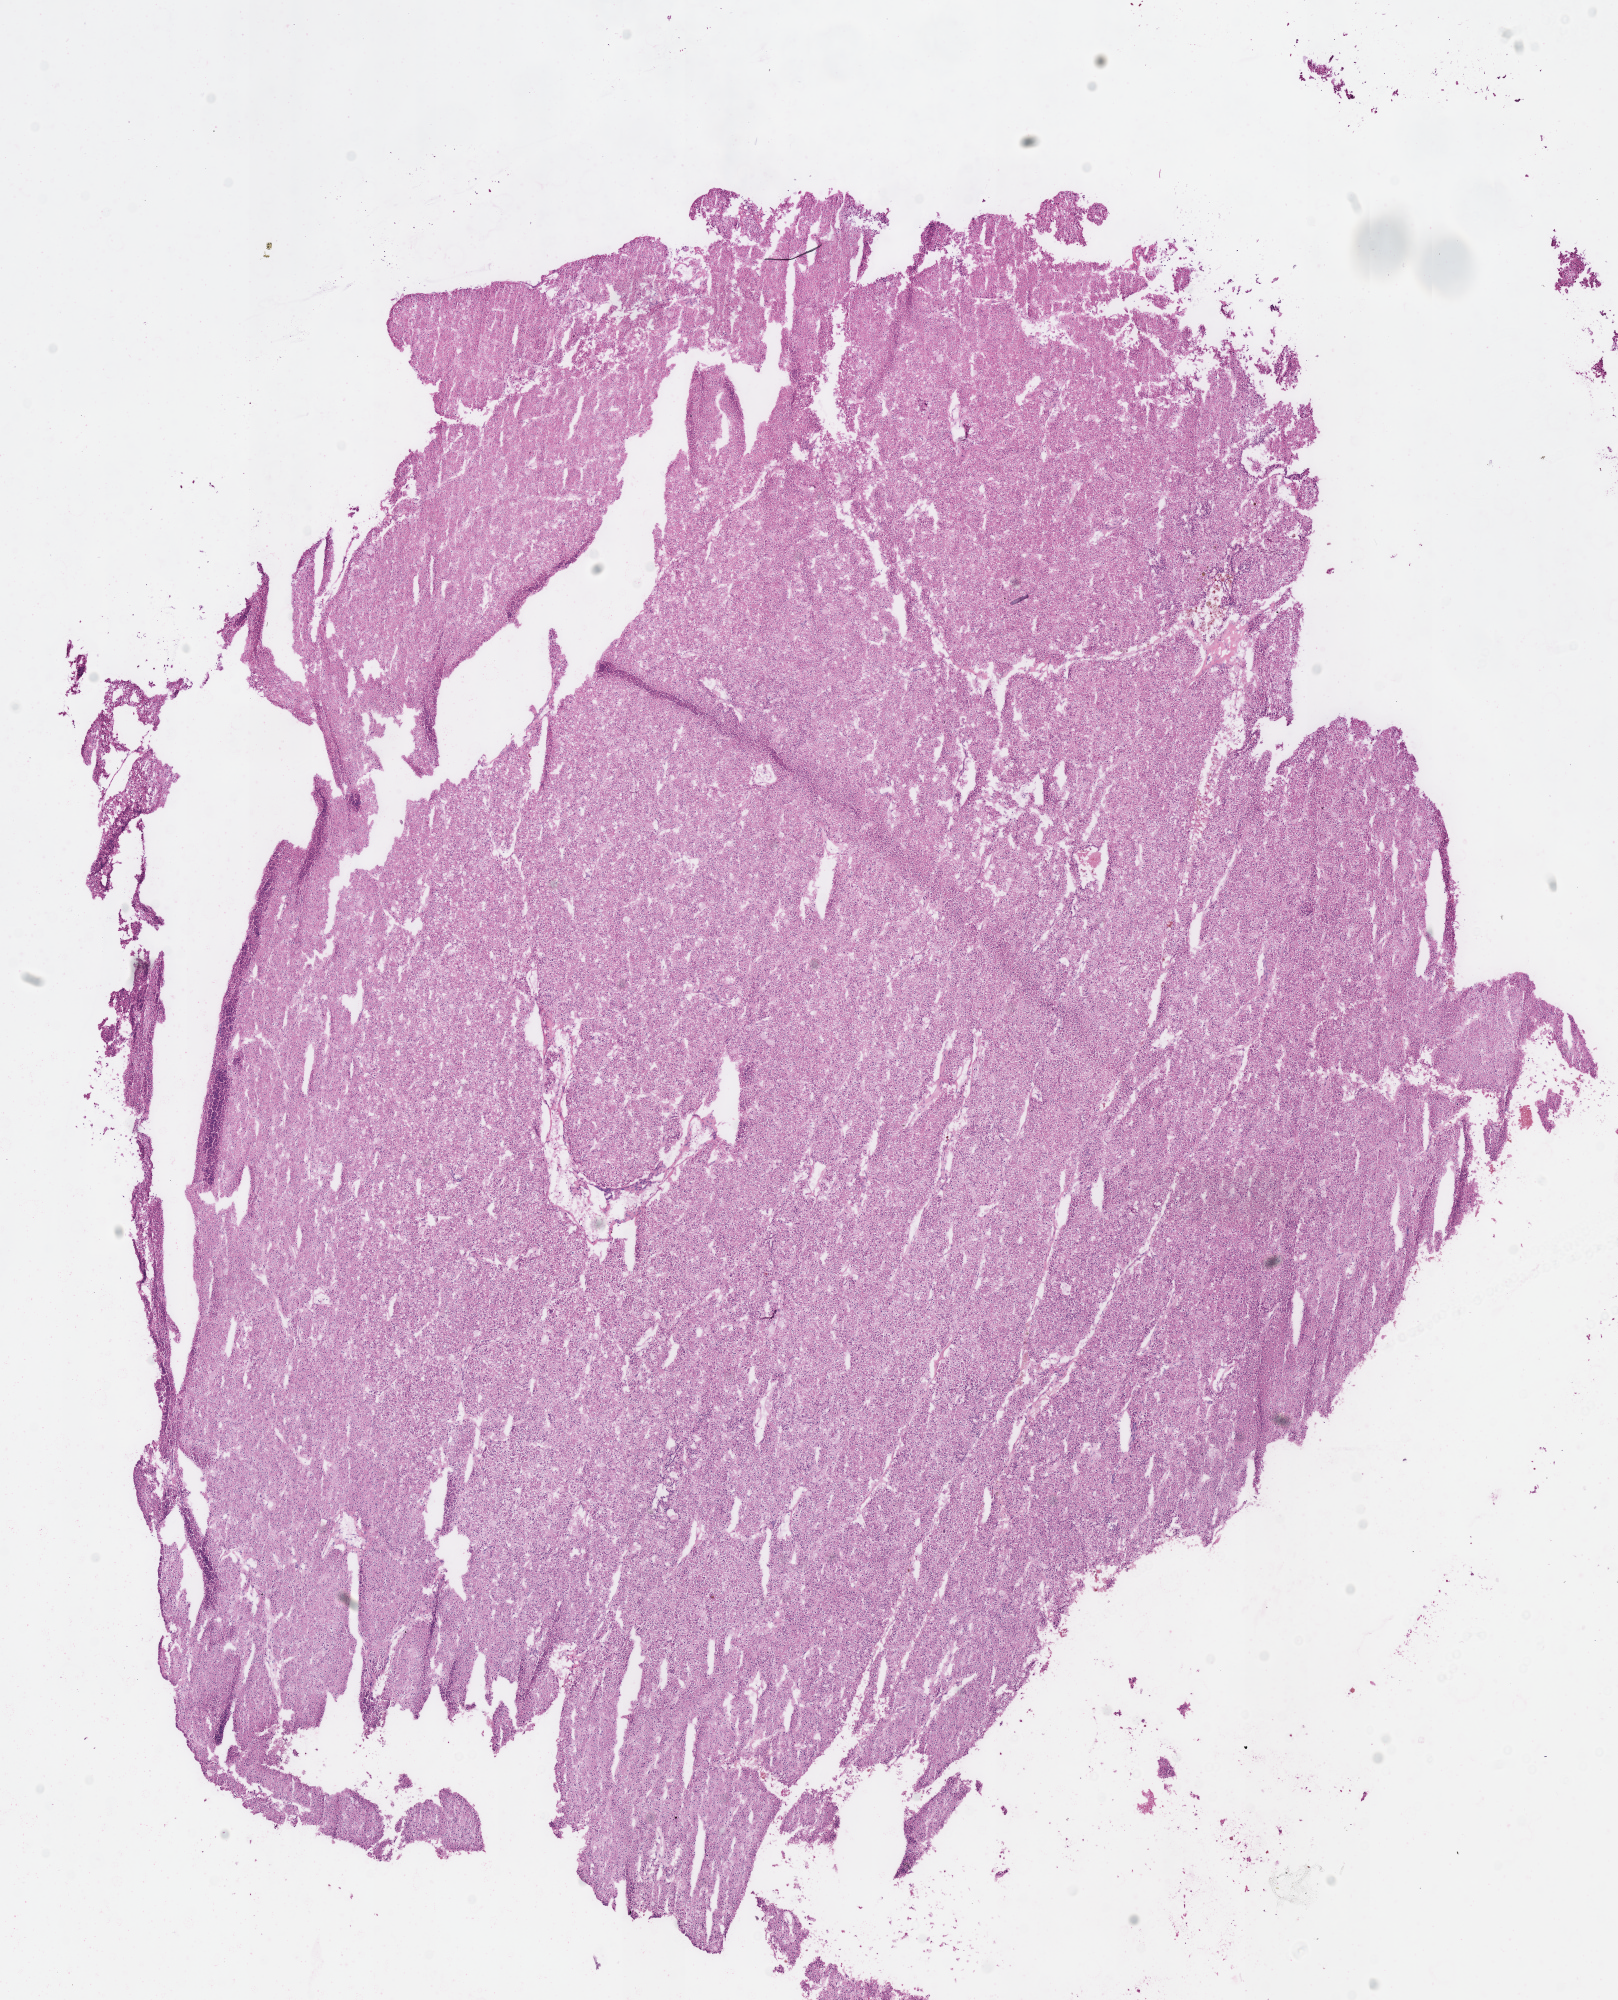
H&E-stained whole-slide image, a low-resolution overview of the entire scanned area, about 12.7 x 15.7 mm. Frozen section. Primary tumour sample from the kidney. Male, age 57 years at initial diagnosis. Pathologist review of this section (percent, as recorded): tumour cells 90%, tumour nuclei 90%, normal cells 0%, stromal cells 10%, necrosis 0%.
• laterality: right
• AJCC pathologic stage: II (6th edition)
• diagnosis: Renal cell carcinoma, chromophobe type
• TNM: T2 N0 MX